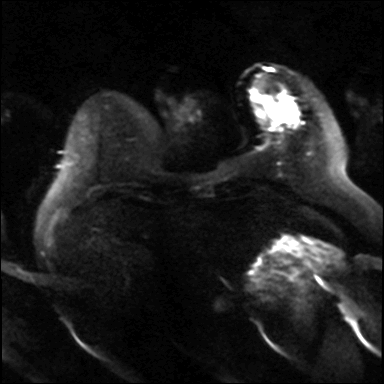
Breast MRI, one axial slice; position 6 of 36 along the scan axis; diffusion-weighted series; image 2 of 4 stored at this slice position (different b-values; order by instance number); 3 T; 4 mm slice thickness; 384 × 384 image matrix. Female patient.
Outlined on this slice (expert manual segmentation):
- tumour on diffusion-weighted imaging: box from (x=268, y=104) to (x=298, y=124) px